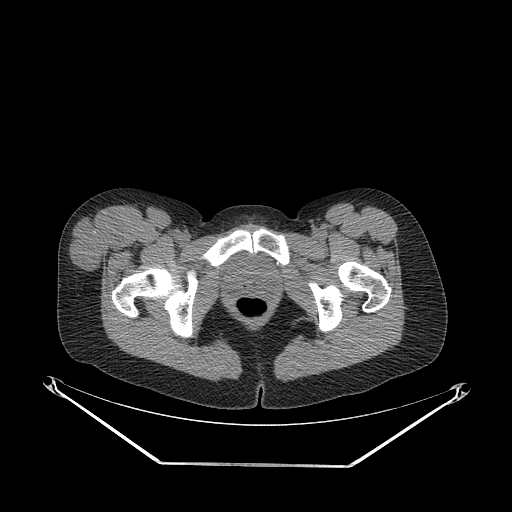
CT of an extremity soft-tissue mass (from a PET/CT study), one axial slice. Slice 61 of 267 in the series (ordered by position). 140 kVp. Soft-tissue window (W 400 / L 40 HU). 512 × 512 image matrix, field of view 500 × 500 mm. Female patient. From the clinical record (not read from this slice): histological type: synovial sarcoma; grade: intermediate; site of the primary tumour: right thigh.
Annotated regions visible in this slice (expert contour drawn on MRI and transferred to this co-registered scan by the dataset authors):
- gross tumour volume including surrounding oedema: bounding box (x1, y1, x2, y2) in pixels: (69, 212, 124, 273)
- gross tumour volume (mass): (69, 212, 124, 273)